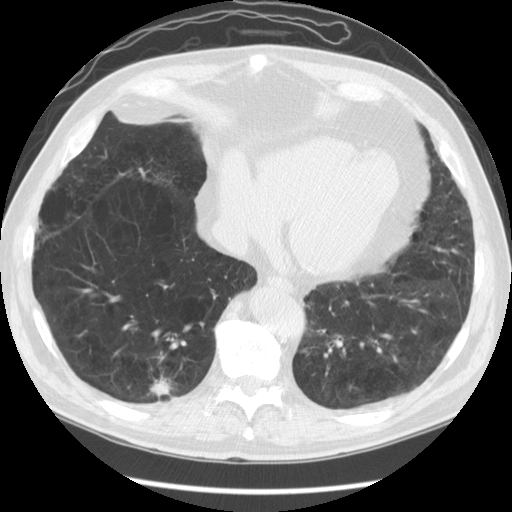
Chest CT (low-dose screening protocol), one axial image; baseline annual screen; lung window (W 1500 / L -600 HU); 2.5 mm slice thickness; slice 98 of 141 in the series; 512 × 512 image matrix, field of view 370 × 370 mm. Male participant, aged 67 years at enrolment. Former smoker at enrolment.
Expert-annotated lung lesion, bounding box (x1, y1, x2, y2) in pixels: (120, 356, 186, 416). The screening reader recorded 2 non-calcified nodules or masses ≥4 mm on this exam (right lower lobe, right lower lobe); which of them this box marks is not recorded.